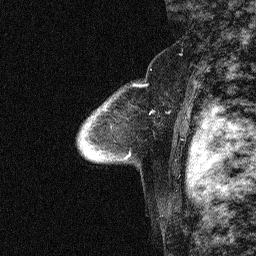
Breast MRI (dynamic contrast-enhanced), one sagittal slice; slice 47 of 64 in the series (ordered by position); dynamic contrast-enhanced study with each time point stored as its own series, time point 2 of 3 at this slice position (early post-contrast, ordered by acquisition time); 1.5 T; TE 4.5 ms, TR 11 ms; 256 × 256 image matrix. Patient: female, 46 years. Case-level facts recorded for this patient, not image findings: setting: breast cancer imaged before/during neoadjuvant chemotherapy; receptor status: HER2-positive.
Outlined on this slice (semi-automatic segmentation, software-assisted and operator-edited):
- analysis volume of interest (the breast-tissue region the enhancement analysis was run in; not a lesion): bounding box <49,51,180,169> (left, top, right, bottom; pixels)
- tumour enhancement mask (voxels above the 90 % enhancement threshold inside the analysis volume of interest): <152,111,169,112>